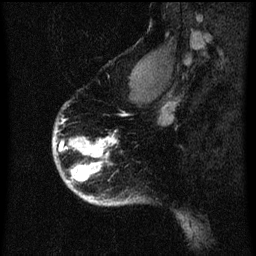
Breast MRI (dynamic contrast-enhanced), one sagittal slice. Position 50 of 60 along the scan axis. Dynamic contrast-enhanced series, image 2 of 3 at this slice position (ordered by acquisition). 1.5 T. TE 4.2 ms, TR 8 ms. 256 × 256 image matrix, field of view 180 × 180 mm. Female patient, age 56 years.
Structures marked on this image (semi-automatically segmented with operator editing):
- analysis volume of interest (the breast-tissue region the enhancement analysis was run in; not a lesion): bounding box (x1, y1, x2, y2) in pixels: (54, 106, 125, 207)
- tumour enhancement mask (voxels above the 70 % enhancement threshold inside the analysis volume of interest): (54, 138, 117, 205)